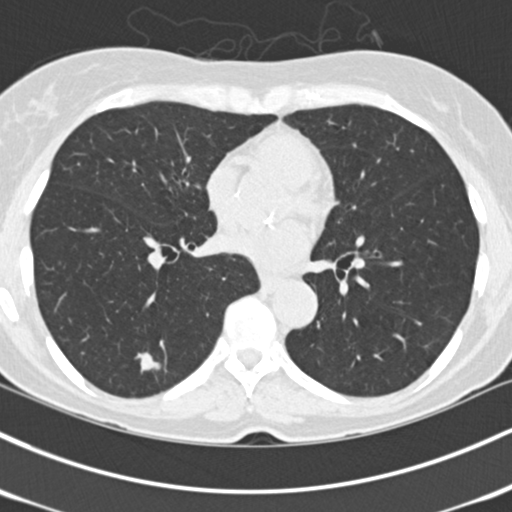
Low-dose screening chest CT, one axial slice; reconstruction kernel B30f; lung window (W 1500 / L -600 HU); 2 mm slice thickness; 512 × 512 image matrix, field of view 318 × 318 mm.
Outlined on this slice (outlined manually by an expert reader):
- lesion 1 (tumor): bounding box (x1, y1, x2, y2) in pixels: (136, 353, 160, 372)